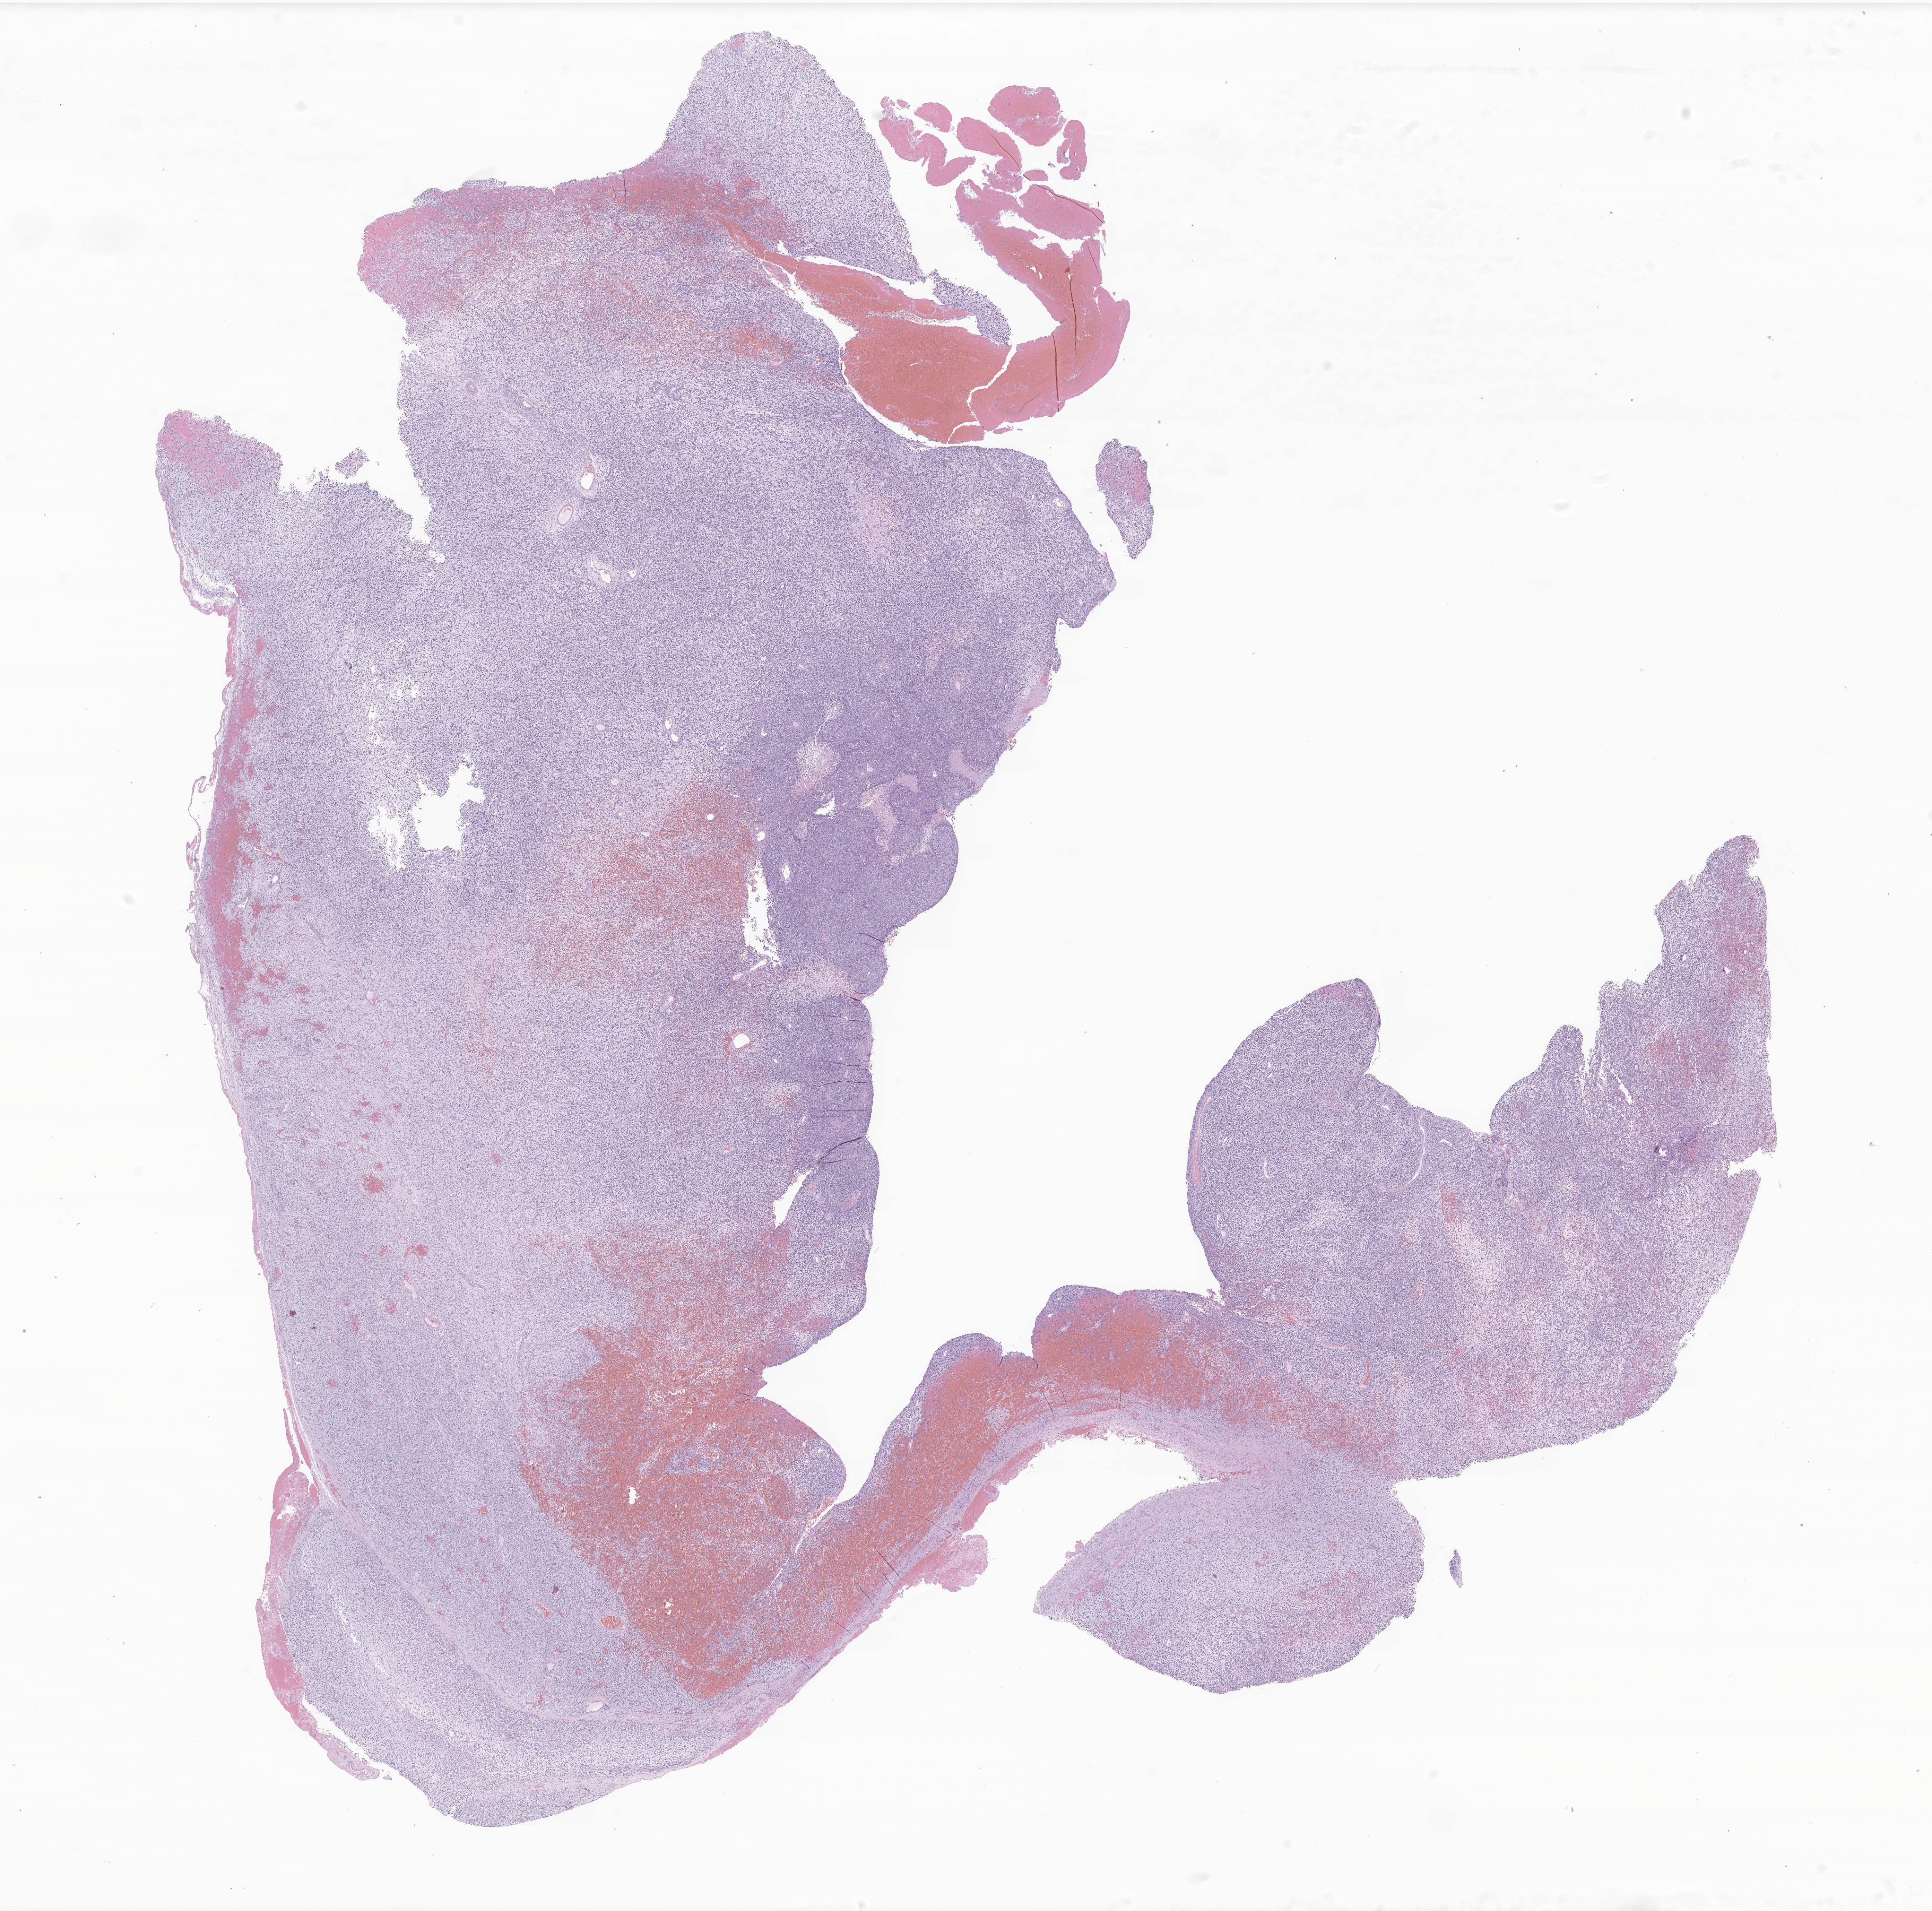
Whole-slide image, H&E stain of tumor tissue from the orbit, low-resolution overview of the scanned area, about 23.5 x 23.2 mm, formalin-fixed paraffin-embedded section. Female patient, age 86 months (7 years 2 months).
- recorded diagnosis: Rhabdomyosarcoma, NOS